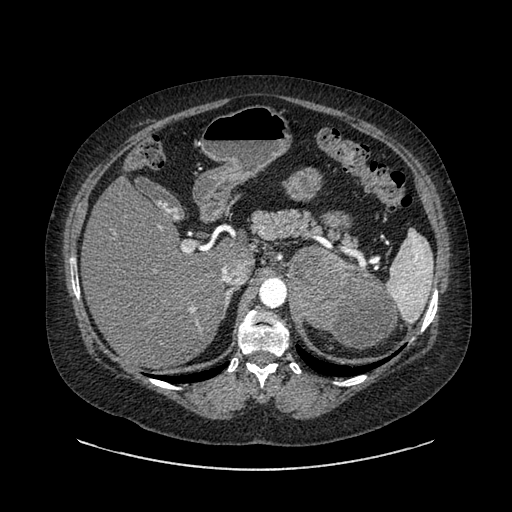
Contrast-enhanced abdominal CT, one axial slice. Position 595 of 769 along the scan axis. Reconstruction kernel SOFT. Intravenous contrast given. Soft-tissue window (W 400 / L 40 HU). 0.62 mm slice thickness. 512 × 512 image matrix, field of view 460 × 460 mm. Patient: female, 61 years. From the clinical record (not read from this slice): diagnosis: adrenocortical carcinoma; tumour side: left adrenal; tumour size at pathology: 13 cm; Ki-67 index: 79 %; stage (as recorded): 2.
Structures marked on this image (semi-automatic segmentation, software-assisted and operator-edited):
- mass: bounding box (x1, y1, x2, y2) in pixels: (288, 249, 394, 350)